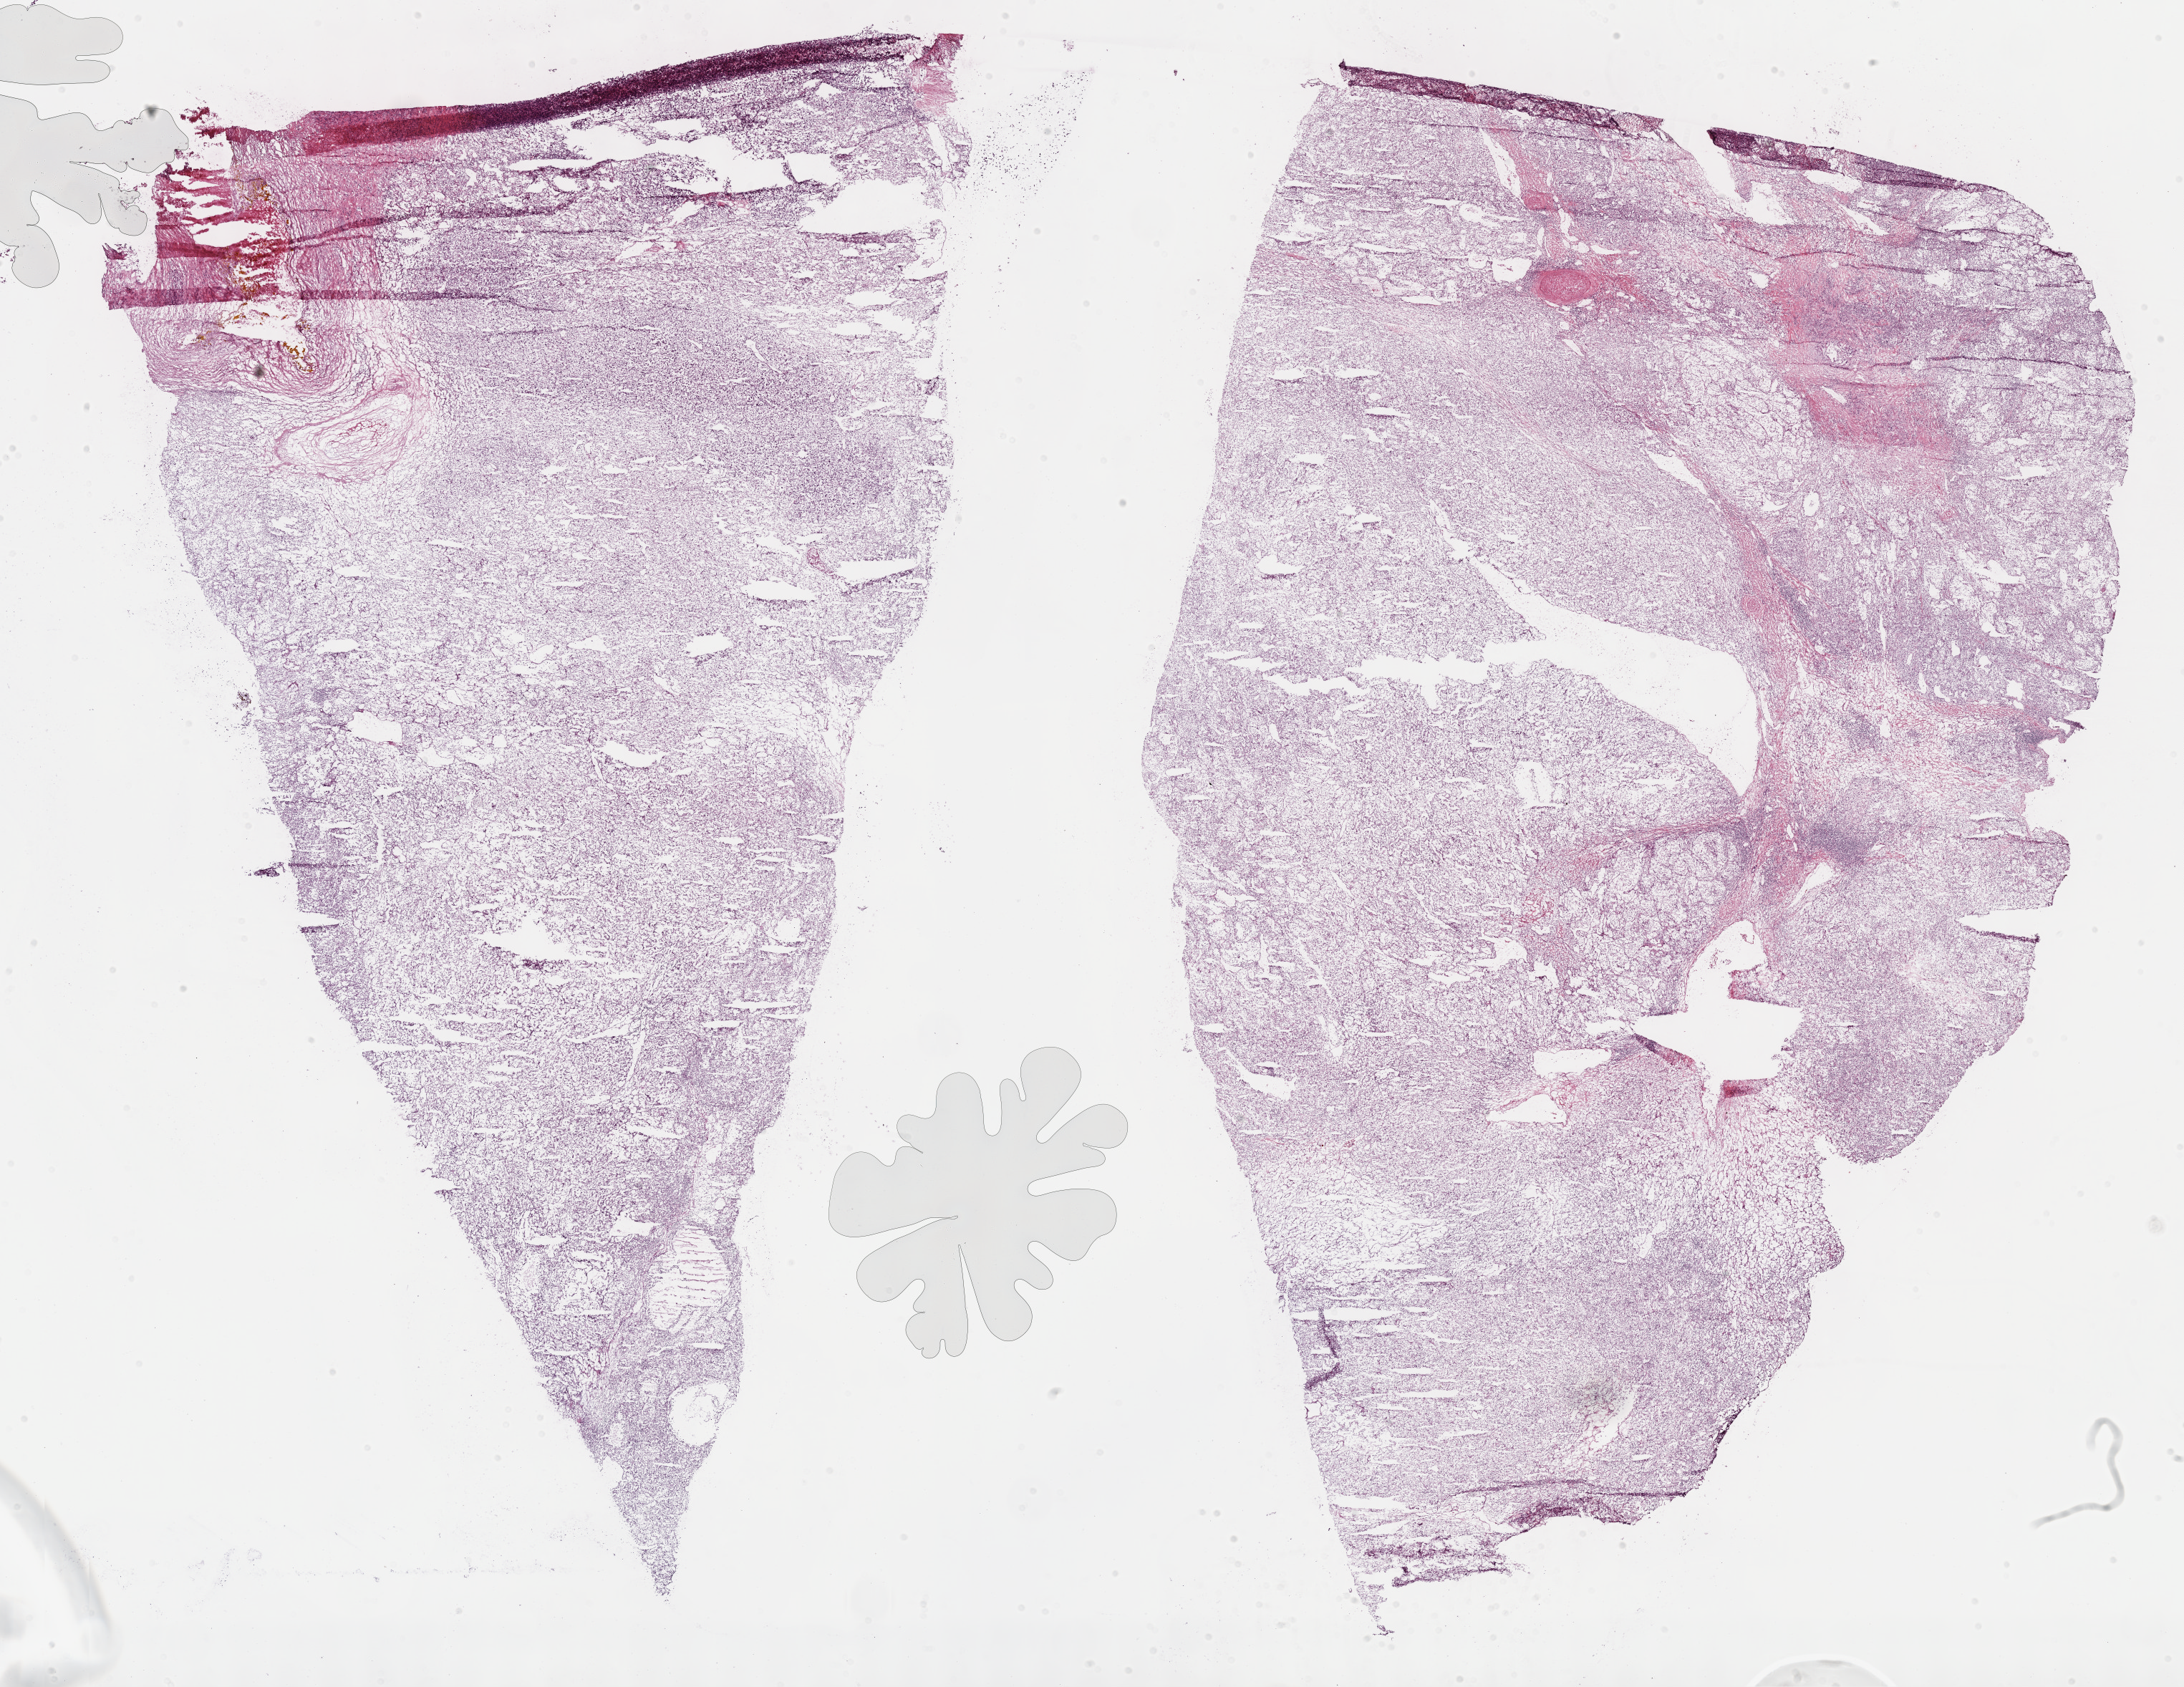
Digitized H&E tissue section (whole slide), low-resolution overview of the scanned area, about 24.7 x 19.1 mm, frozen section from the top of the tissue portion, sample: primary tumour, kidney. Female patient; age at initial diagnosis 66 years. Histologic grade: G3 (poorly differentiated). Composition of this section per pathologist review: tumour cells 87%, tumour nuclei 85%, normal cells 0%, stromal cells 10%, necrosis 3%.
Lymph nodes positive (case pathology): 0 of 1 examined. AJCC pathologic stage: IV. Laterality: left. Diagnosis: Clear cell adenocarcinoma, NOS.